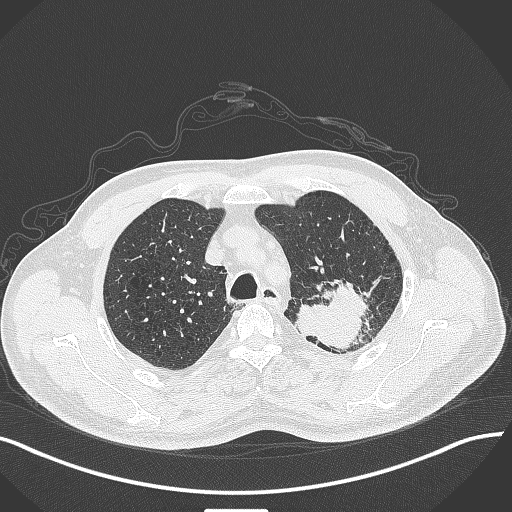
Chest CT, one axial slice. Slice 333 of 429 in the series (ordered by position). Reconstruction kernel B70f. Lung window (W 1500 / L -600 HU). 1 mm slice thickness. 512 × 512 image matrix, field of view 400 × 400 mm. Patient: male, 55 years. Case-level facts recorded for this patient, not image findings: clinical TNM (as recorded): T3 N0 M1c; histopathological grade: G3.
Outlined on this slice (rectangle marked by the reading radiologist):
- lung tumour (recorded histology: adenocarcinoma): bounding box [x1, y1, x2, y2] px = [298, 277, 376, 350]